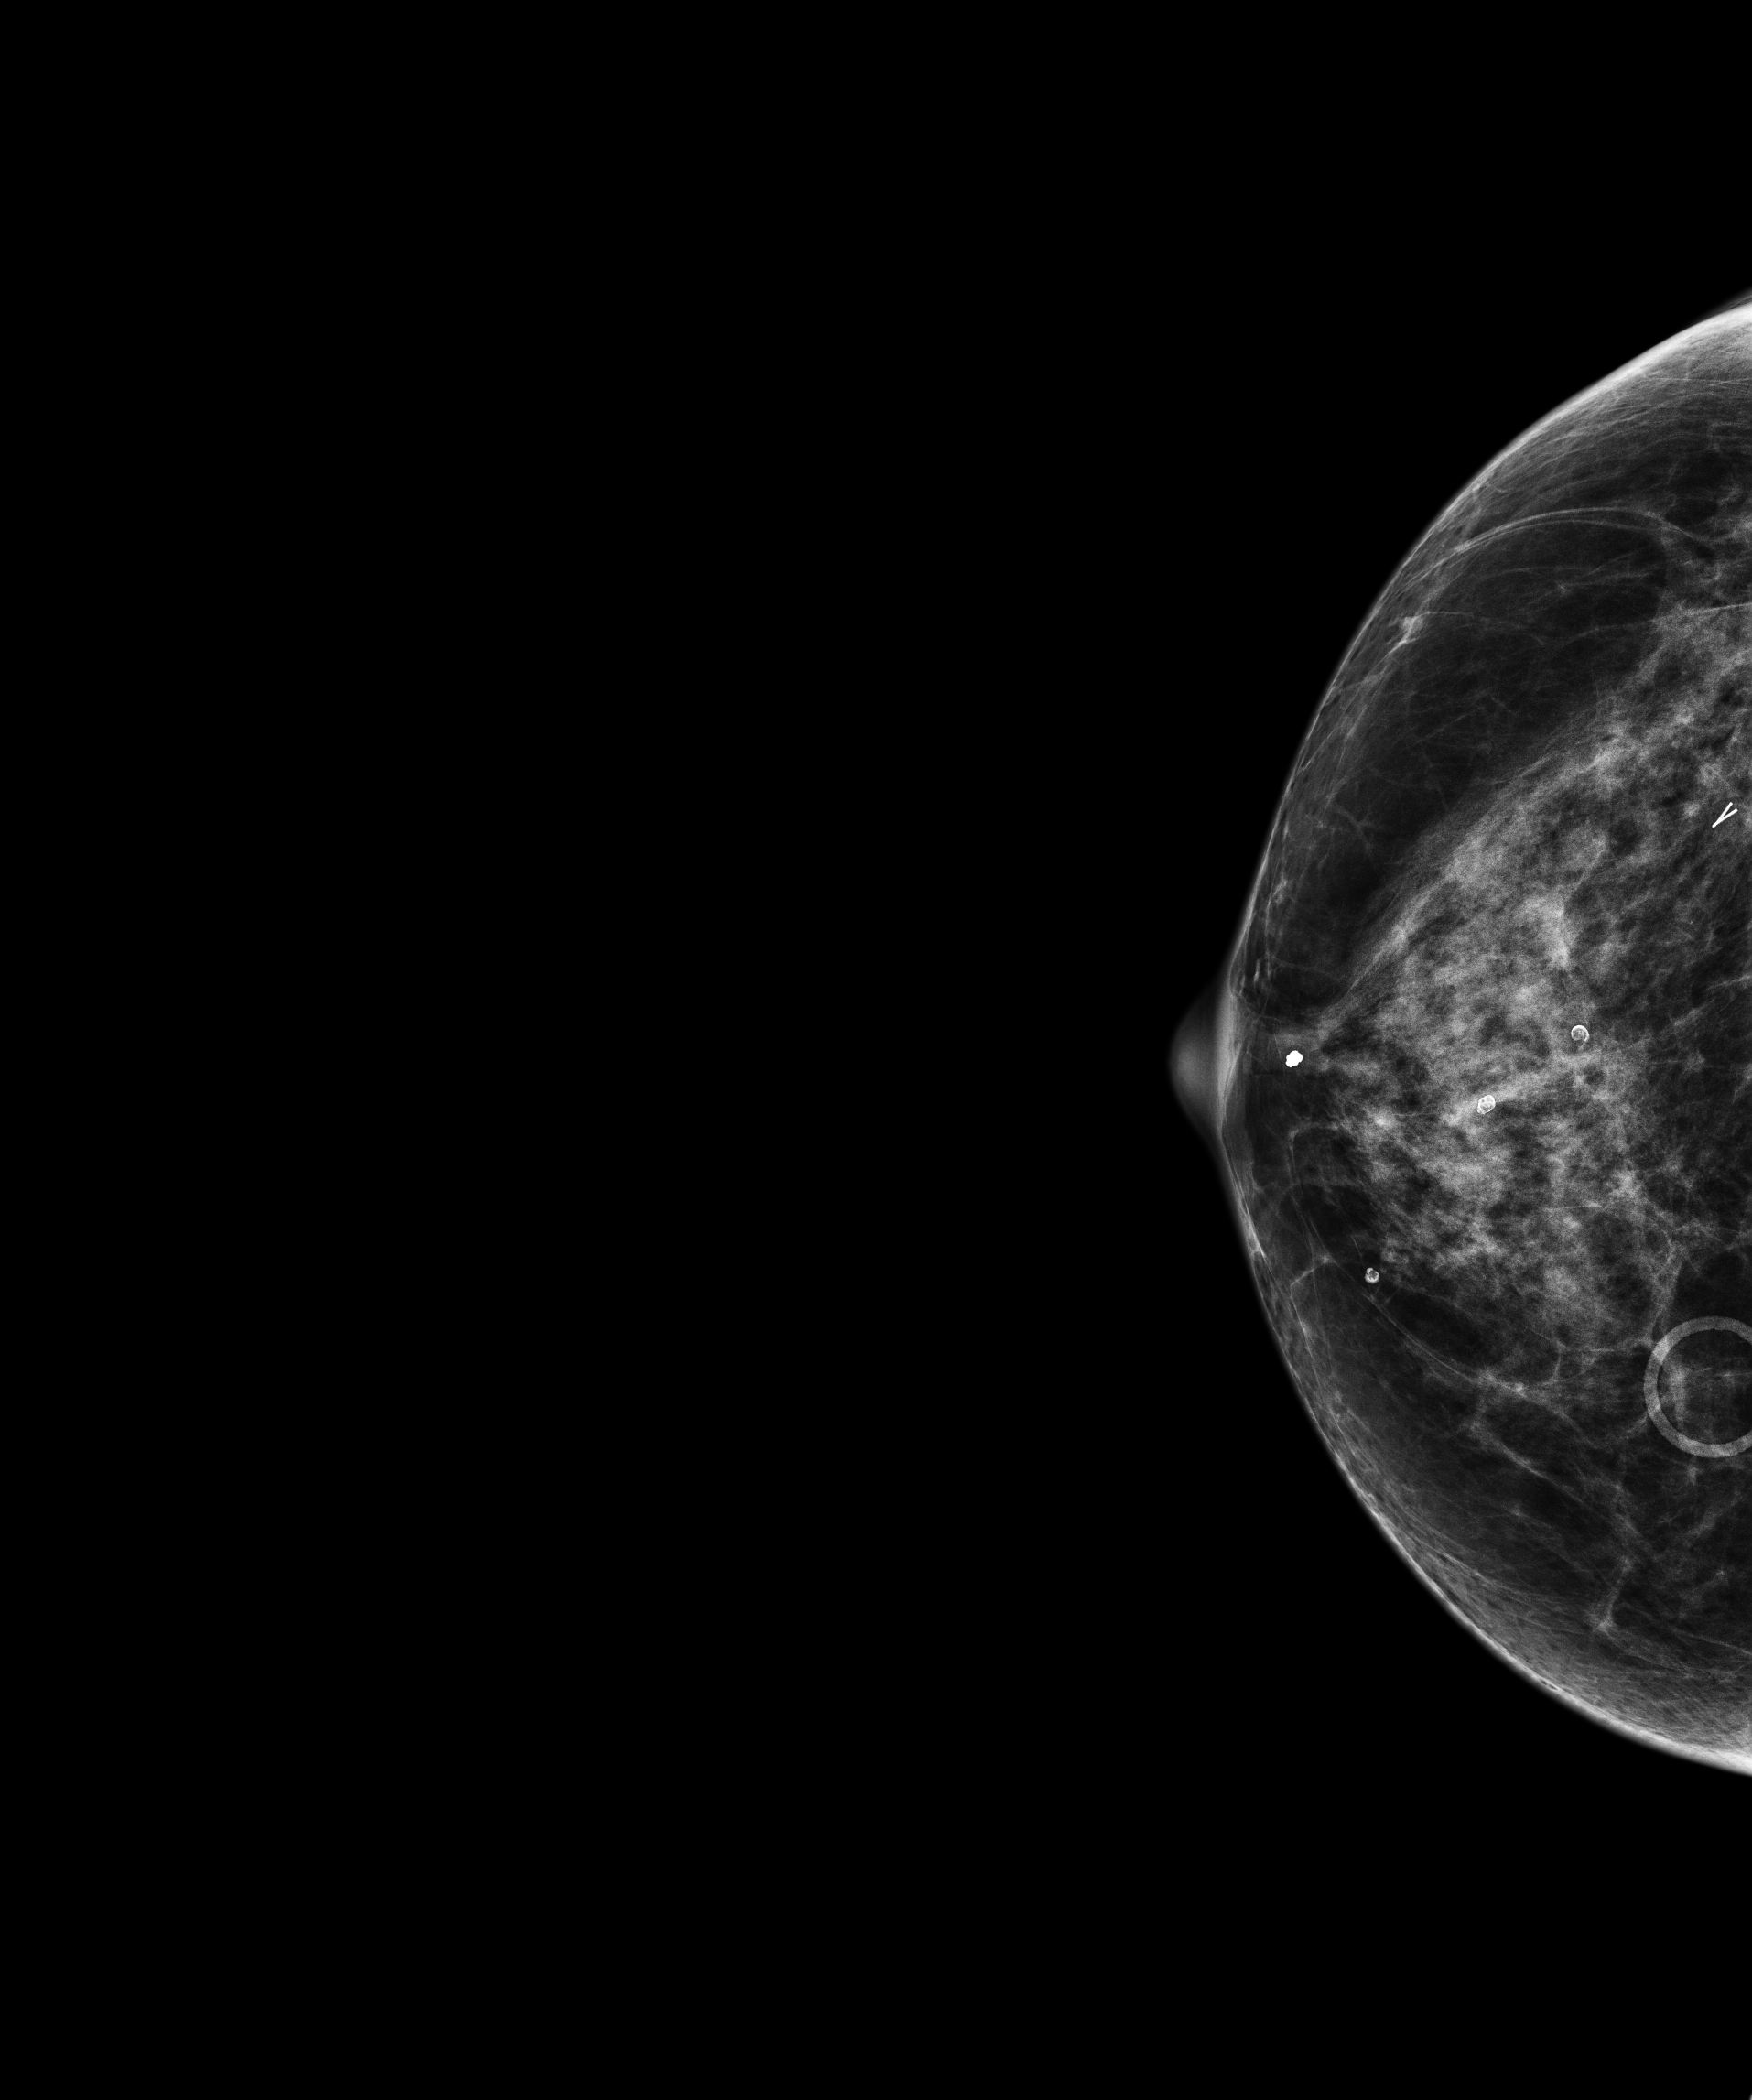
Screening examination. Patient: female, 65 years.
Image type: full-field digital mammogram. Breast: right. Projection: craniocaudal (CC) view.